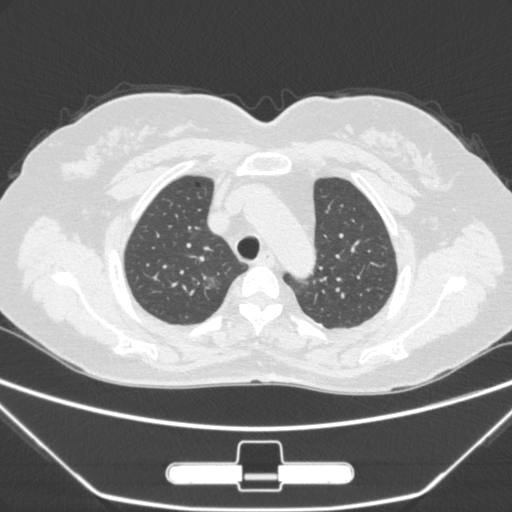
Chest CT, one axial slice. Position 223 of 275 along the scan axis. 120 kVp. Lung window (W 1500 / L -600 HU). 1 mm slice thickness. 512 × 512 image matrix, field of view 356 × 356 mm. Patient: female, 63 years. Case-level facts recorded for this patient, not image findings: clinical TNM (as recorded): T1a N0 M0; histopathological grade: G1.
Structures marked on this image (bounding box drawn by a radiologist):
- lung tumour (recorded histology: adenocarcinoma): bounding box [x1, y1, x2, y2] px = [195, 268, 236, 311]